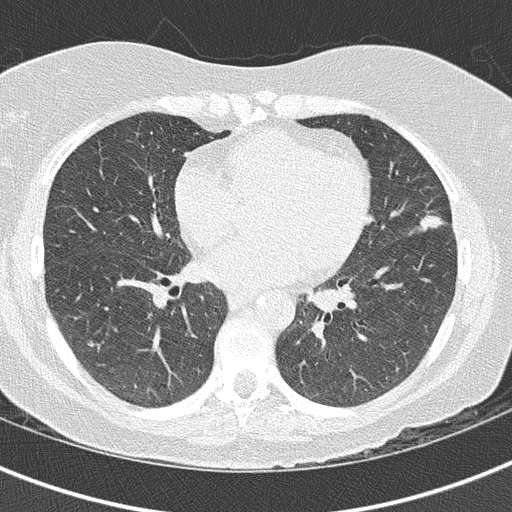
Low-dose screening chest CT, axial slice, third annual screen, lung window (W 1500 / L -600 HU), 2 mm slice thickness, lung (sharp) reconstruction kernel (B50f), slice 79 of 158 in the series. Female participant, aged 63 years at enrolment.
- Lesion marked by an expert reader, bounding box (x1, y1, x2, y2) in pixels: (387, 197, 455, 248).
- The screening reader recorded 5 non-calcified nodules or masses ≥4 mm on this exam (lingula, left lower lobe, right upper lobe, right upper lobe, right upper lobe); which of them this box marks is not recorded.
- Official screen result: positive, other.
- Participant outcome: lung cancer diagnosed 35 days after this screen — bronchiolo-alveolar adenocarcinoma, NOS, lingula, stage IA (AJCC 6th edition), 14 mm at pathology.